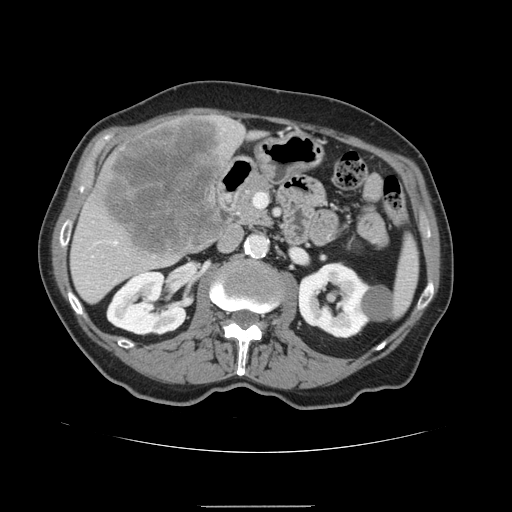
Contrast-enhanced abdominal CT, one axial slice; slice 67 of 168 in the series (ordered by position); intravenous contrast given; soft-tissue window (W 400 / L 40 HU); 2.5 mm slice thickness; 512 × 512 image matrix. Male patient, age 74 years. From the clinical record (not read from this slice): diagnosis: colorectal cancer liver metastases, imaged before liver resection; multiple liver metastases: no; largest metastasis: 14.5 cm.
Annotated regions visible in this slice (manually delineated by an expert):
- liver: bounding box <70,115,250,305> (left, top, right, bottom; pixels)
- planned liver remnant (the part of the liver to remain after resection): <74,276,114,305>
- liver metastasis: <104,118,228,258>